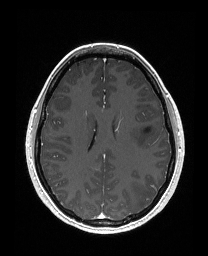
Brain MRI from a brain-tumour surgery series, one axial slice. Slice 102 of 176 in the series (ordered by position). T1-weighted post-contrast. 1 mm slice thickness. 208 × 256 image matrix, field of view 203 × 250 mm. Case-level facts recorded for this patient, not image findings: histopathology: Astrocytoma; WHO grade: 3; IDH mutation: yes; tumour location: Left Frontal.
Structures marked on this image (outlined manually by an expert reader):
- tumour: box from (x=129, y=122) to (x=158, y=148) px